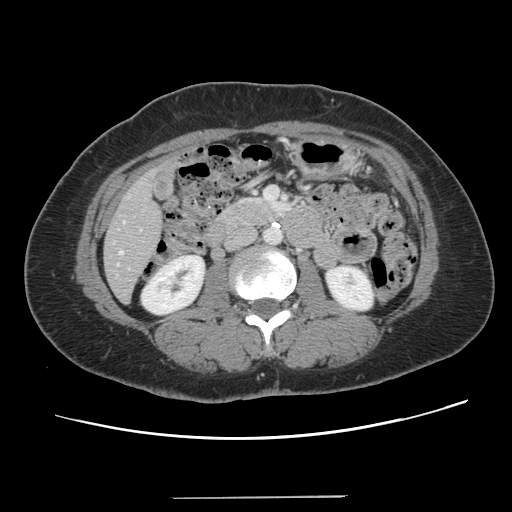
Contrast-enhanced abdominal CT, one axial slice. Slice 40 of 141 in the series (ordered by position). 120 kVp. Intravenous contrast given. Soft-tissue window (W 400 / L 40 HU). 512 × 512 image matrix, field of view 366 × 366 mm. Female patient, age 53 years. From the clinical record (not read from this slice): diagnosis: colorectal cancer liver metastases, imaged before liver resection; multiple liver metastases: no; largest metastasis: 14.5 cm; chemotherapy before resection: yes.
Annotated regions visible in this slice (expert manual segmentation):
- hepatic veins: box from (x=119, y=251) to (x=122, y=254) px
- liver: (x=105, y=167)–(x=161, y=301)
- planned liver remnant (the part of the liver to remain after resection): (x=105, y=215)–(x=161, y=302)